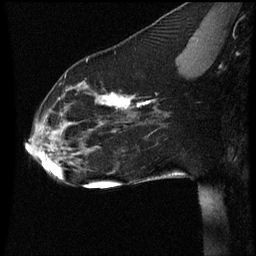
Breast MRI (dynamic contrast-enhanced), one sagittal slice; position 21 of 60 along the scan axis; dynamic contrast-enhanced series, image 2 of 3 at this slice position (ordered by acquisition); 1.5 T; TE 4.2 ms, TR 8.9 ms; 2 mm slice thickness; 256 × 256 image matrix. Female patient, age 35 years. From the clinical record (not read from this slice): setting: breast cancer imaged before/during neoadjuvant chemotherapy; receptor status: HER2-positive.
Structures marked on this image (semi-automatically segmented with operator editing):
- analysis volume of interest (the breast-tissue region the enhancement analysis was run in; not a lesion): bounding box [x1, y1, x2, y2] px = [24, 66, 177, 177]
- tumour enhancement mask (voxels above the 70 % enhancement threshold inside the analysis volume of interest): [42, 92, 150, 155]